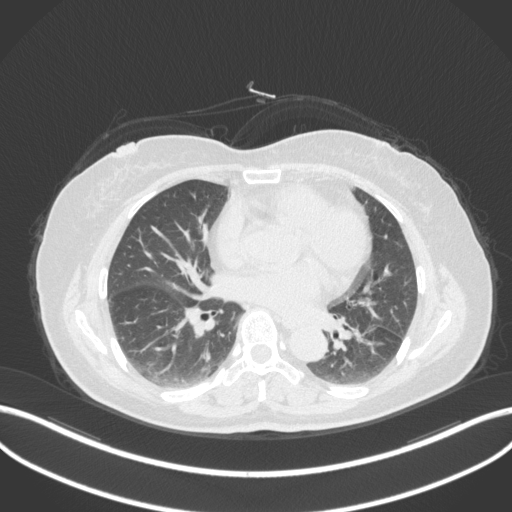
Chest CT, one axial slice. Slice 173 of 307 in the series (ordered by position). Reconstruction kernel B31f. Lung window (W 1500 / L -600 HU). 1 mm slice thickness. 512 × 512 image matrix, field of view 400 × 400 mm. Patient: female, 59 years. Case-level facts recorded for this patient, not image findings: clinical TNM (as recorded): T2a N0 M0; histopathological grade: G2-3.
Structures marked on this image (rectangle marked by the reading radiologist):
- lung tumour (recorded histology: adenocarcinoma): bounding box <351,324,384,361> (left, top, right, bottom; pixels)